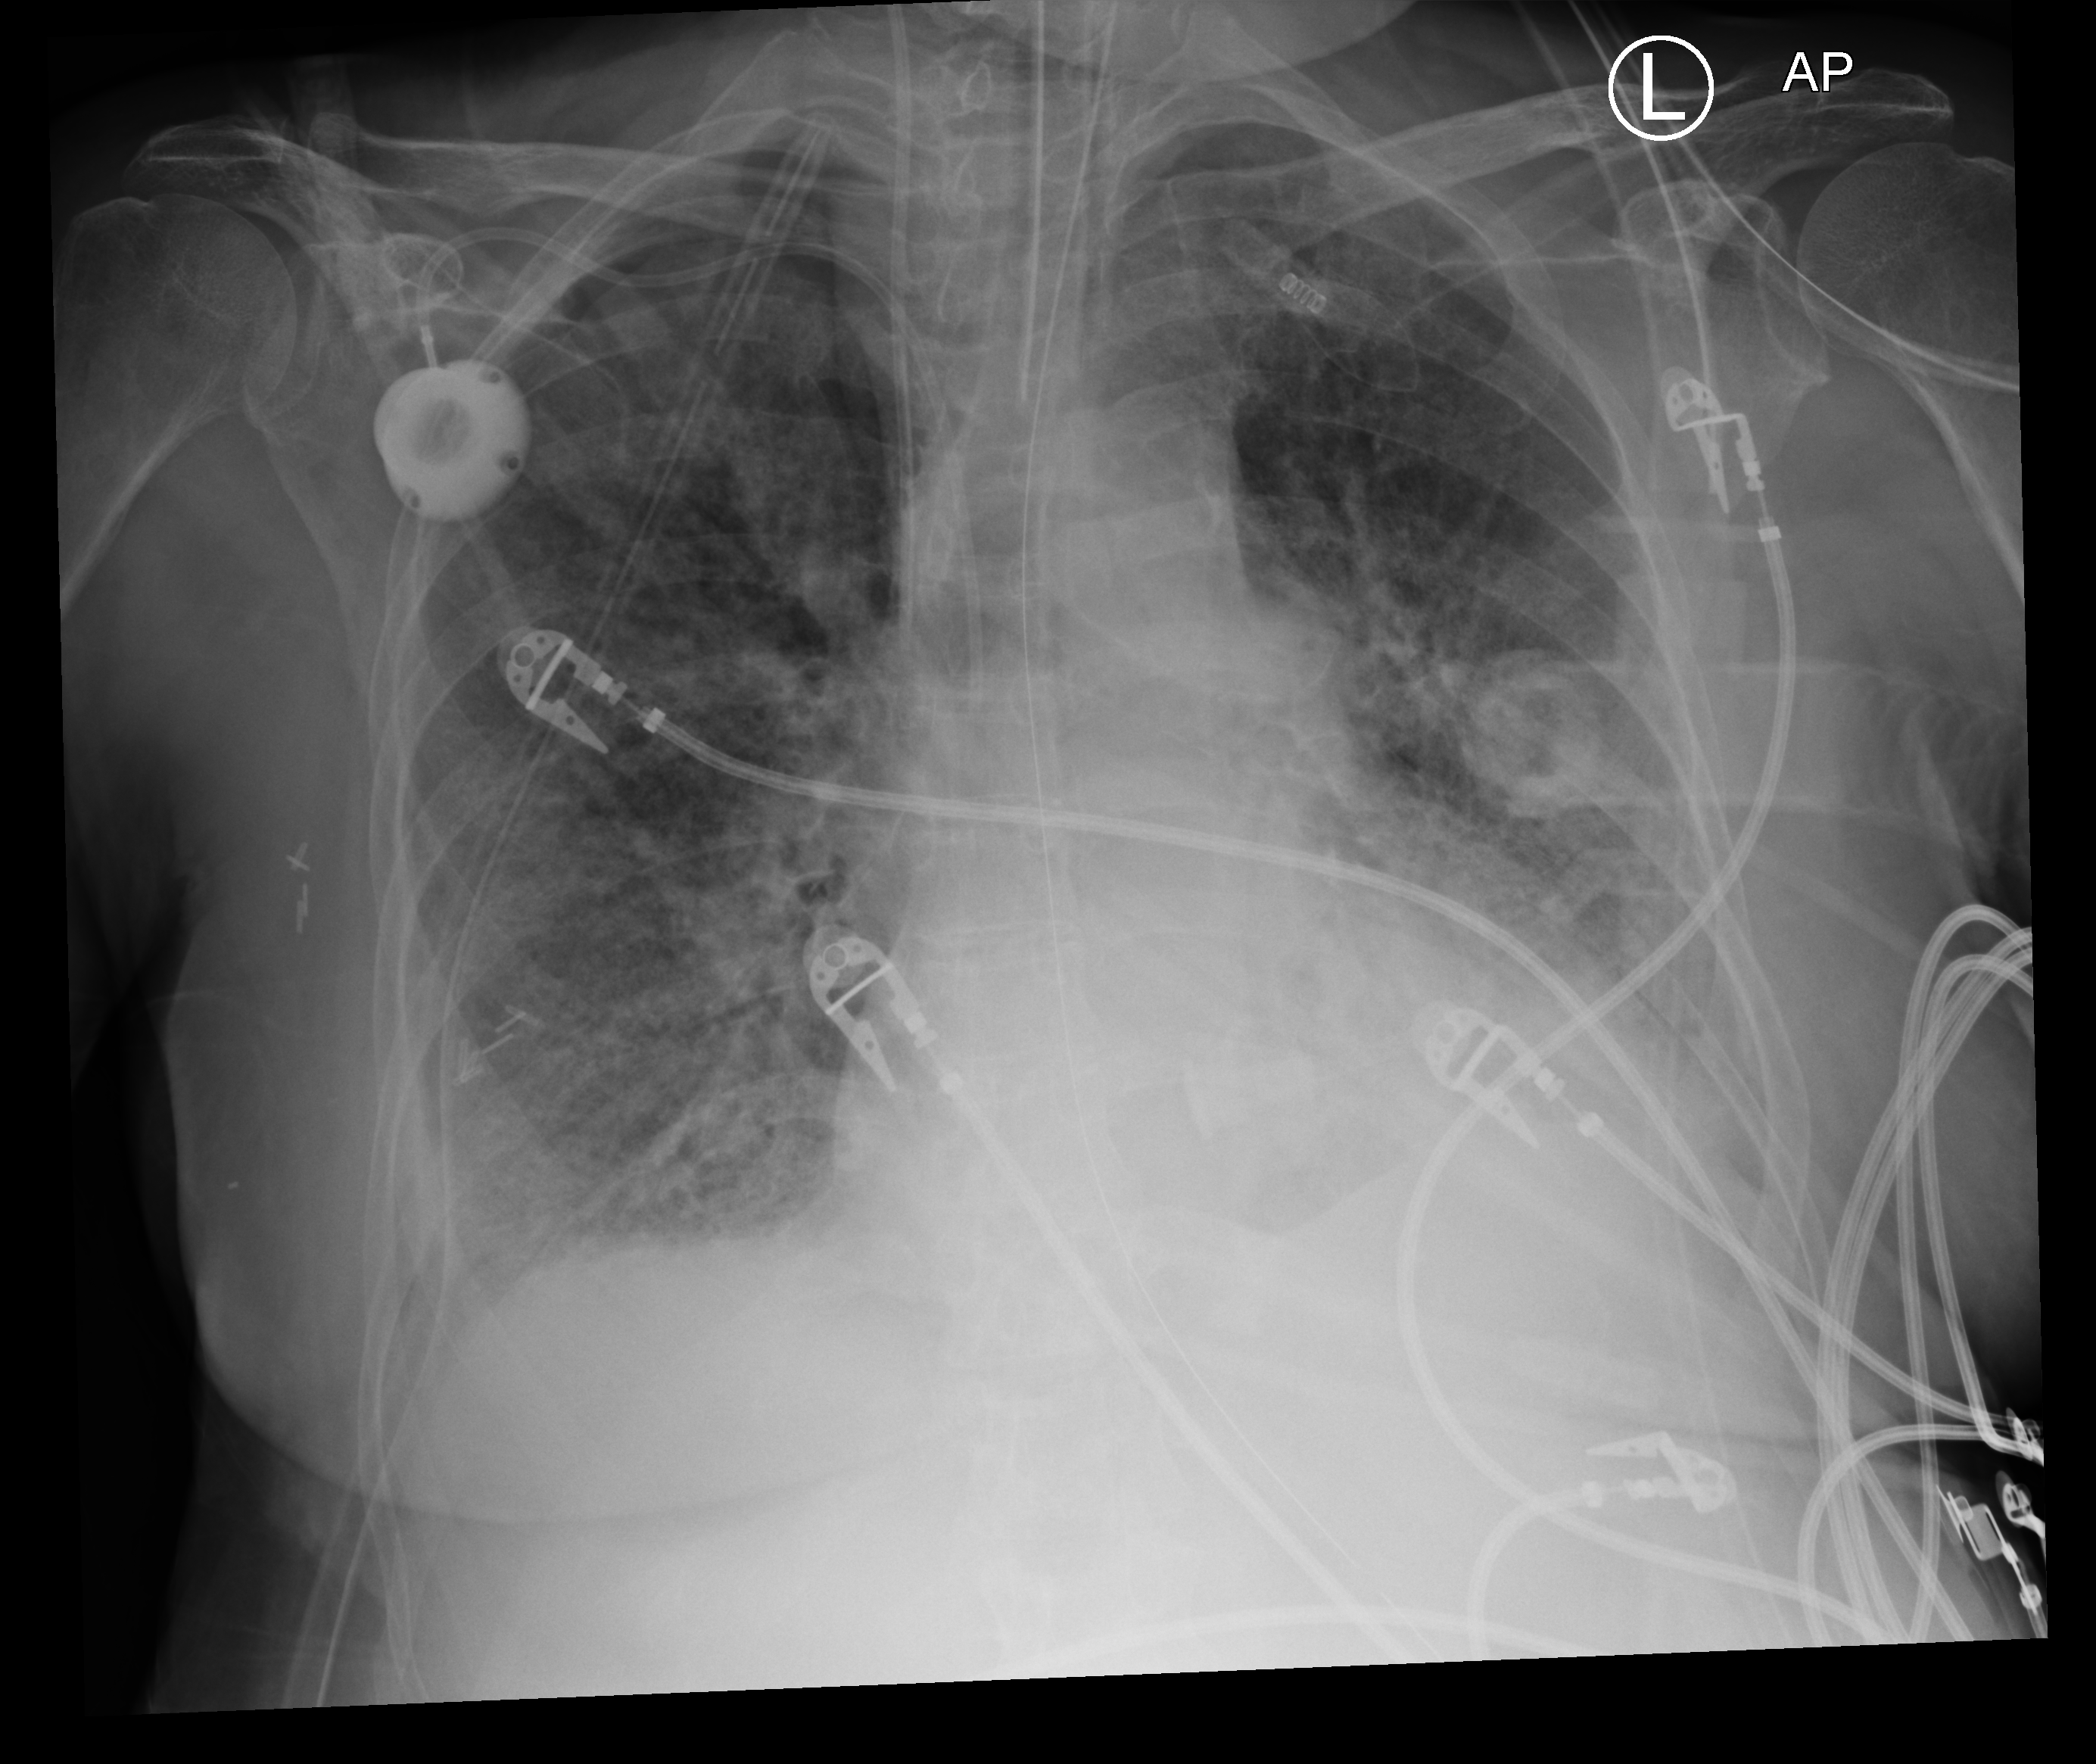
Chest X-ray (portable). Female patient hospitalised with COVID-19, age 60–74 years.
From the hospital-stay record, not from the radiograph (when in the stay this image was taken is not recorded): smoking status (admission record): former.